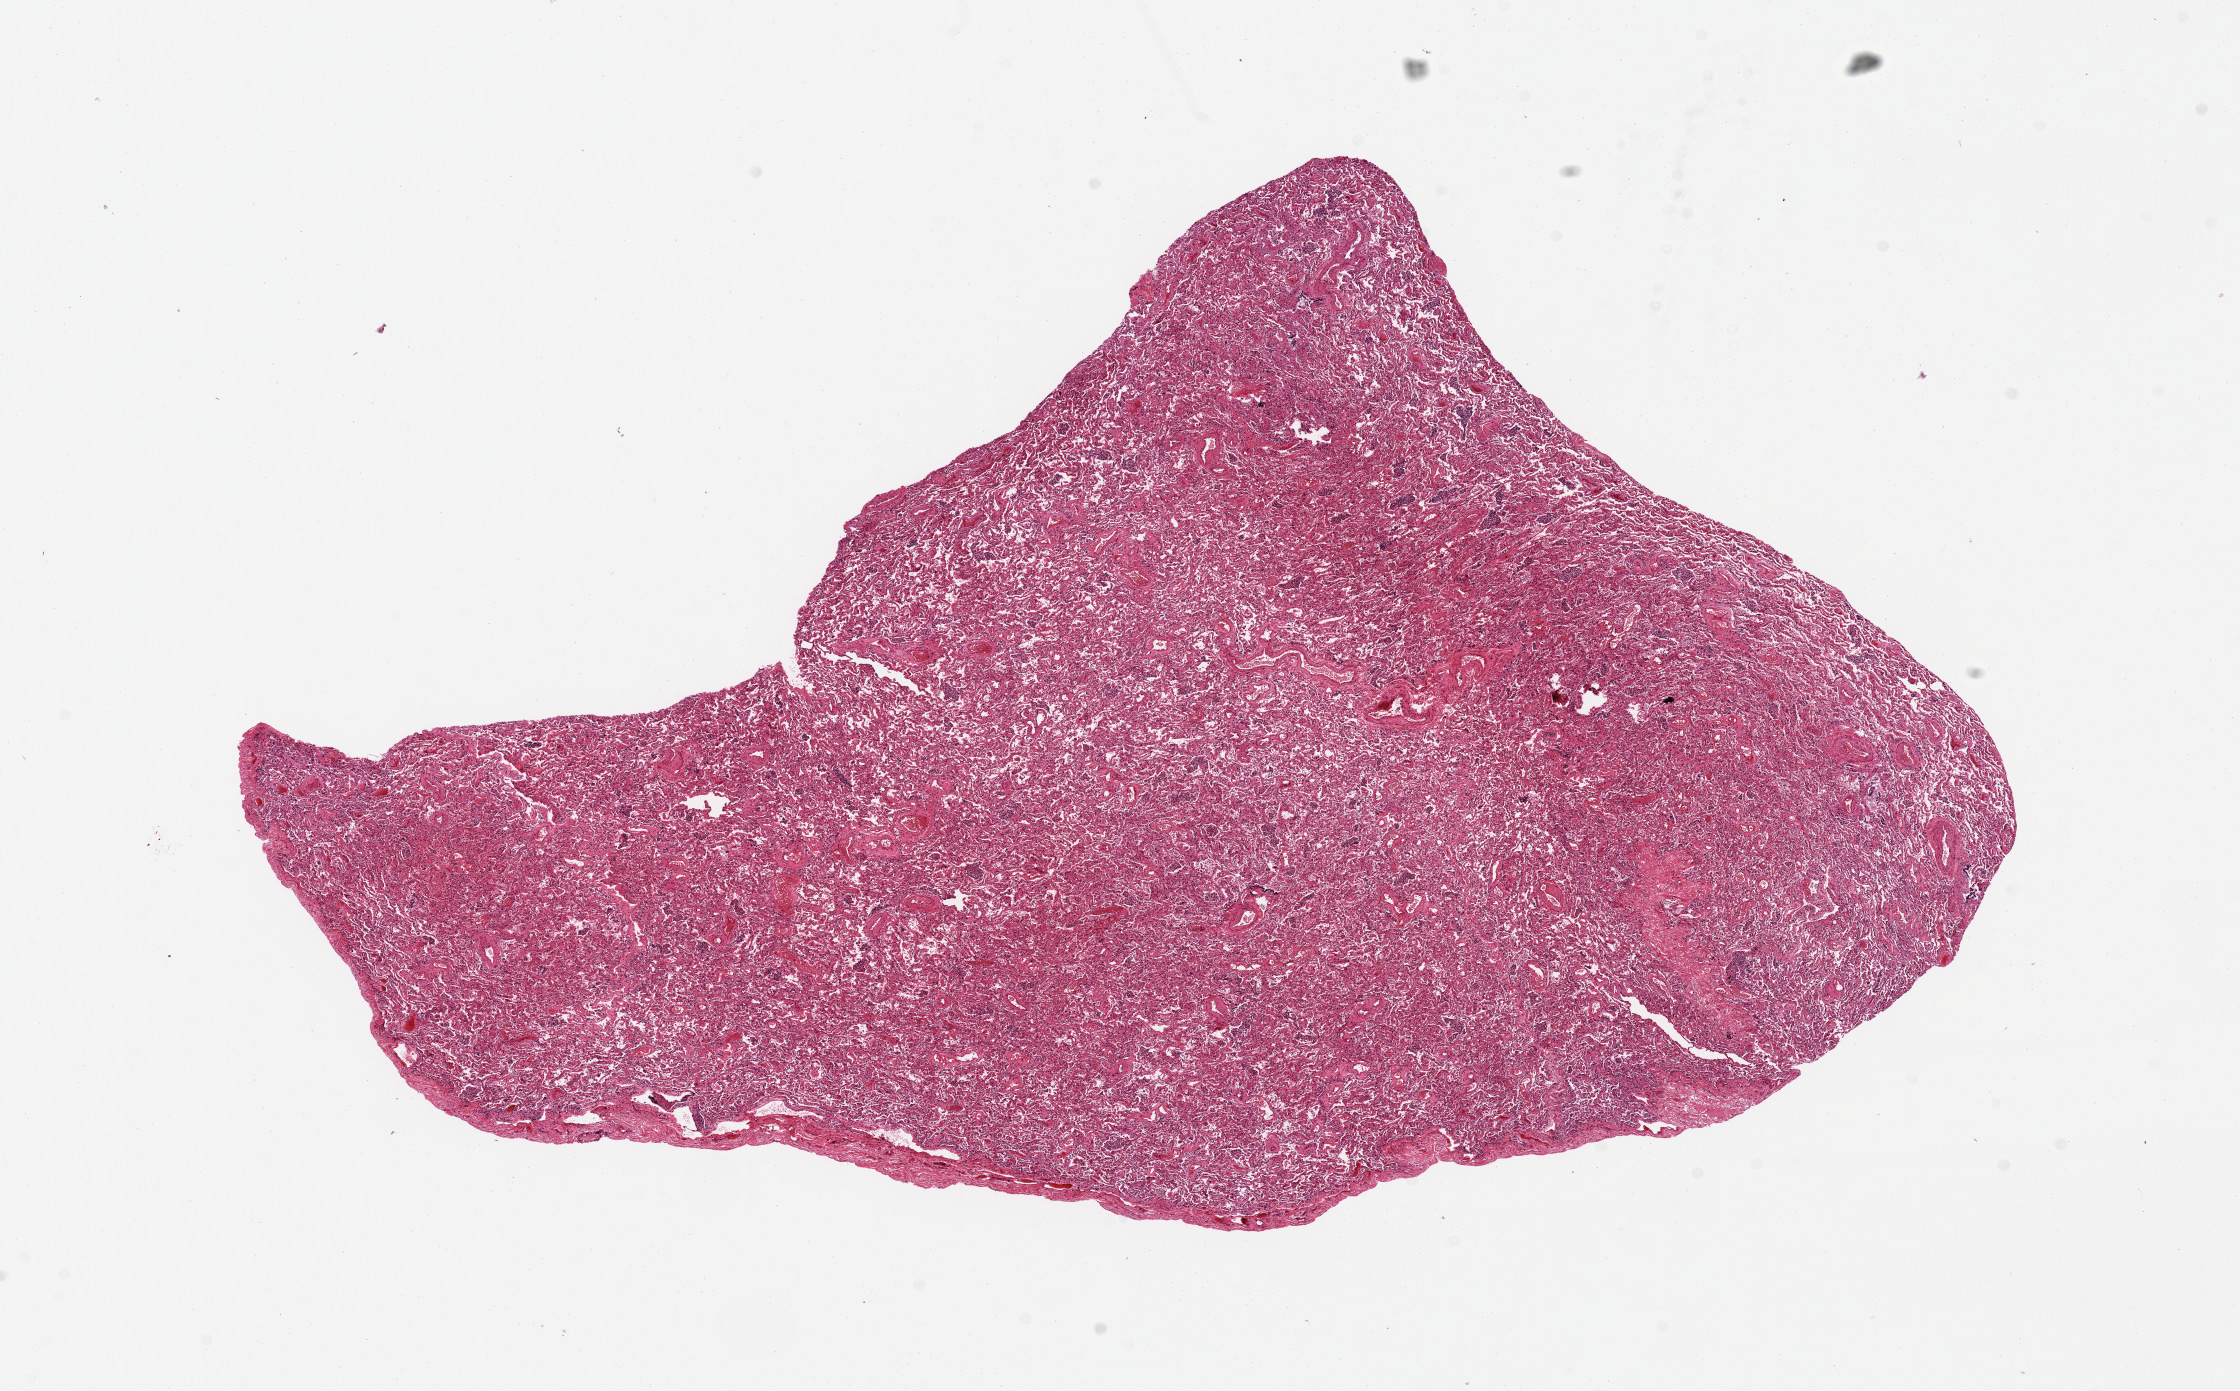
Whole-slide image, H&E stain — low-resolution overview of the scanned area, about 17.7 x 11.0 mm. PAXgene-fixed paraffin-embedded (PFPE) section. Section of lung (target tissue). Donor tissue sample. Donor sex: male.
Pathologist's review note for this sample: Alveolar cellular exudates, possible ventilator damage.